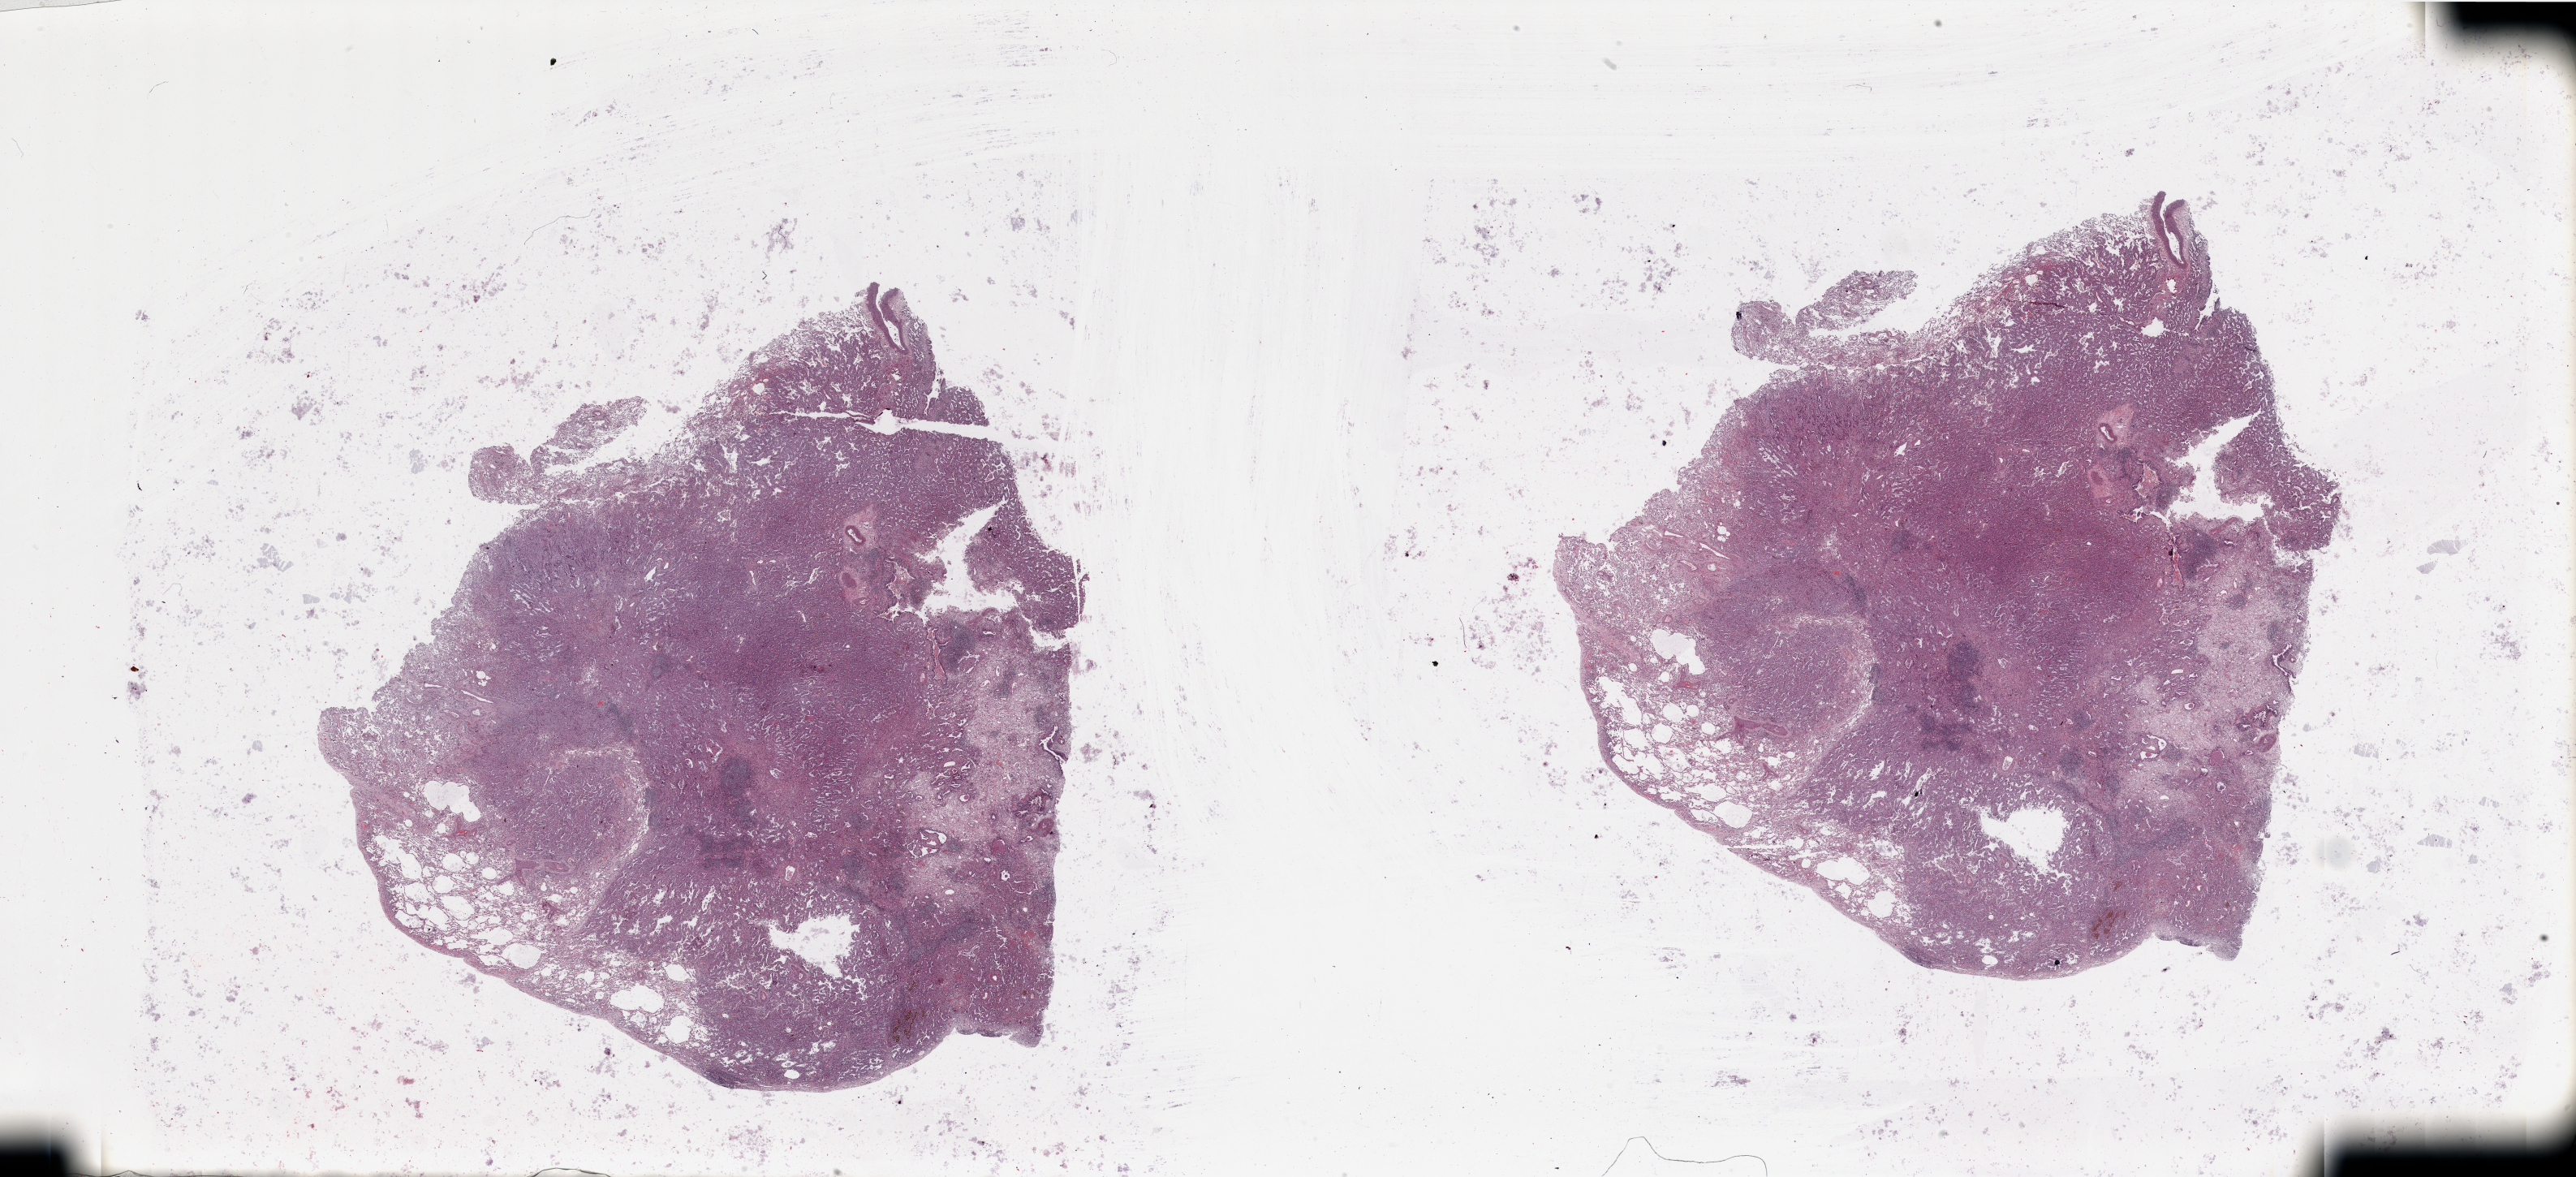
H&E whole-slide image, low-resolution overview of the scanned area, about 50.2 x 22.9 mm, tumour tissue sample, lung. Female, 61 y/o. Histologic grade: G1 (well differentiated).
- histologic diagnosis: Adenocarcinoma, NOS
- AJCC pathologic stage: IA
- primary tumour site (as recorded): right lower lobe